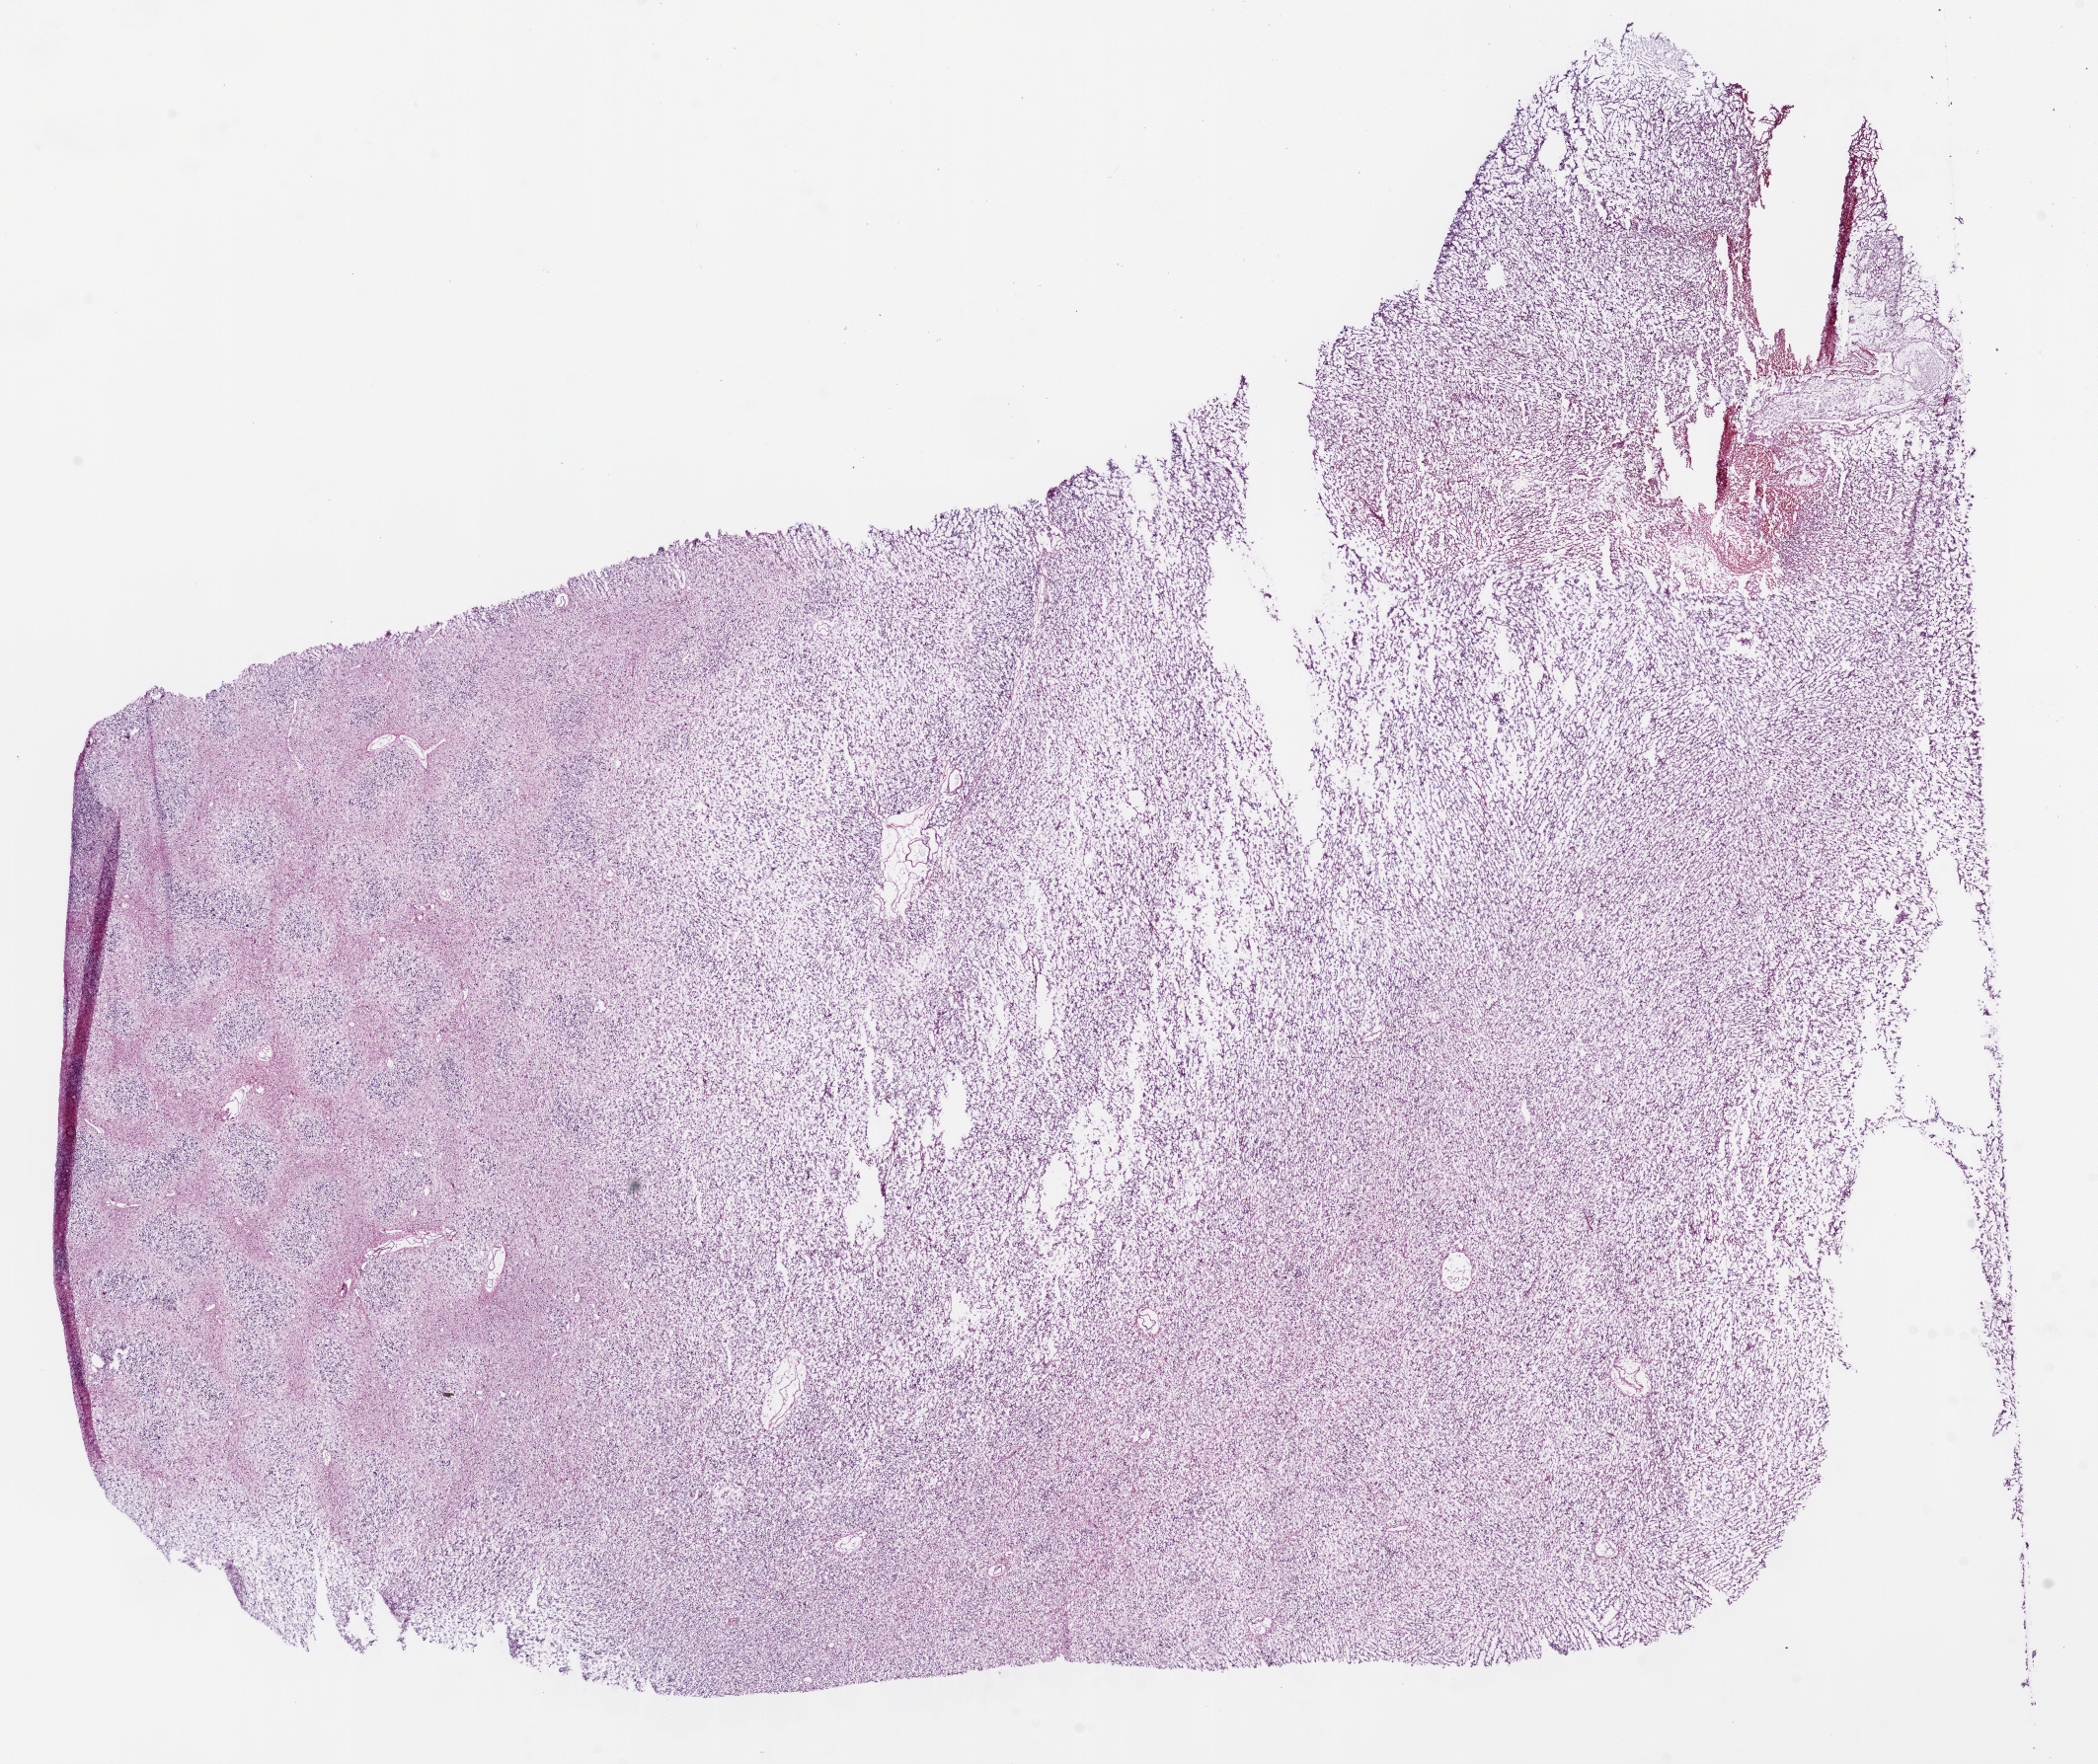
Digitized H&E-stained tissue section (whole slide), whole scanned area (about 17.1 x 14.3 mm, slide scanned at 20x) shown as a low-resolution overview; frozen section; brain, primary tumour sample. Male, age 36 years at initial diagnosis. Histologic grade: G3 (poorly differentiated). Slide review estimates, as recorded: tumour cells 100%, tumour nuclei 65%, normal cells 0%, stromal cells 0%, necrosis 0%.
• pathologic diagnosis: Mixed glioma (cerebrum)